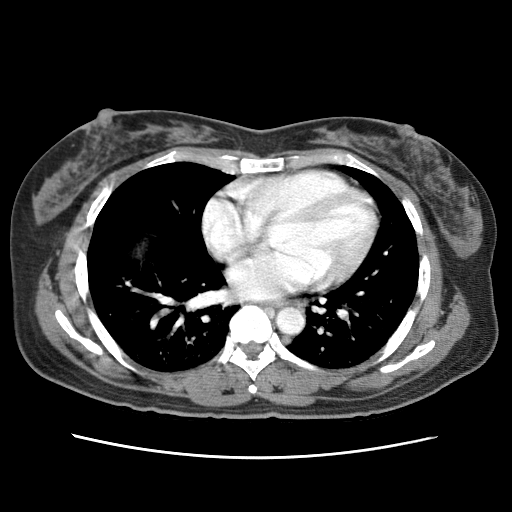
Contrast-enhanced abdominal CT (liver protocol), one axial slice. Position 75 of 79 along the scan axis. Reconstruction kernel STANDARD. 120 kVp. Soft-tissue window (W 400 / L 40 HU). 512 × 512 image matrix. From the clinical record (not read from this slice): diagnosis: hepatocellular carcinoma (patient treated with transarterial chemoembolisation; whether this scan precedes or follows treatment is not stated here); TNM stage (as recorded): Stage-I; Child-Pugh class: A; tumour nodularity: uninodular.
Outlined on this slice (semi-automatically segmented with operator editing):
- abdominal aorta: bounding box (x1, y1, x2, y2) in pixels: (276, 307, 304, 335)